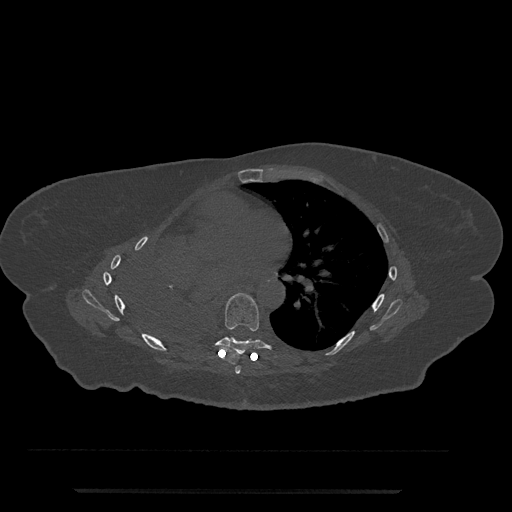
CT including the spine, one axial slice. Position 443 of 797 along the scan axis. Bone window (W 1800 / L 400 HU). 512 × 512 image matrix, field of view 440 × 440 mm. Female patient, age 51 years. From the clinical record (not read from this slice): primary cancer: neuro; vertebrae with lytic lesions (as recorded): T8.
Annotated regions visible in this slice (semi-automatically segmented with operator editing):
- T6 vertebra: bounding box <235,366,241,374> (left, top, right, bottom; pixels)
- T7 vertebra: <207,293,278,355>